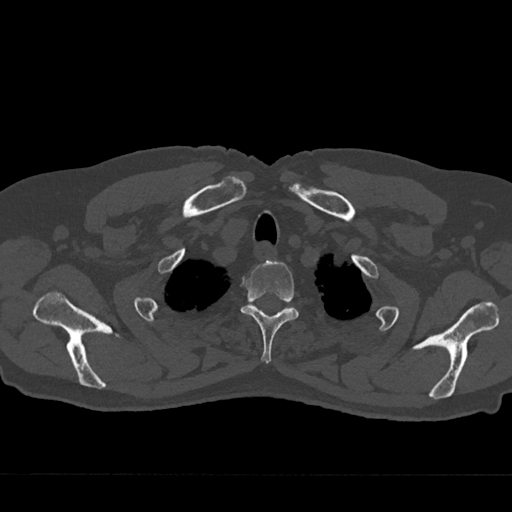
CT including the spine, one axial slice. Slice 610 of 797 in the series (ordered by position). 120 kVp. Bone window (W 1800 / L 400 HU). 0.5 mm slice thickness. 512 × 512 image matrix. Patient: male, 75 years. Case-level facts recorded for this patient, not image findings: primary cancer: renal; vertebrae with lytic lesions (as recorded): T4.
Annotated regions visible in this slice (semi-automatic segmentation, software-assisted and operator-edited):
- T2 vertebra: box from (x=241, y=260) to (x=299, y=363) px